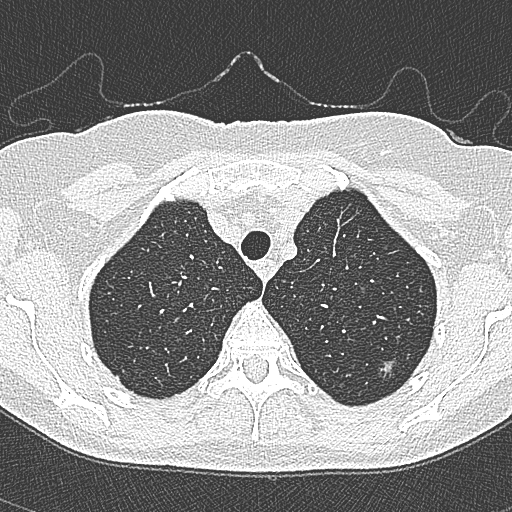
Axial slice from a low-dose chest CT screening exam; second annual screen; lung window (W 1500 / L -600 HU); lung (sharp) reconstruction kernel (B80f). Female, age 65 years at enrolment. Current smoker at enrolment.
Lesion marked by an expert reader, bounding box (x1, y1, x2, y2) in pixels: (366, 348, 408, 386). The screening reader recorded 4 non-calcified nodules or masses ≥4 mm on this exam (left upper lobe, left upper lobe, left upper lobe, right lower lobe); which of them this box marks is not recorded. Official screen result: positive, change unspecified: nodule(s) >= 4 mm or enlarging nodule(s), mass(es), or other non-specific abnormalities suspicious for lung cancer. Lung cancer was diagnosed 54 days after this screen: bronchiolo-alveolar carcinoma, non-mucinous, left upper lobe, stage IA (AJCC 6th edition), 10 mm at pathology.